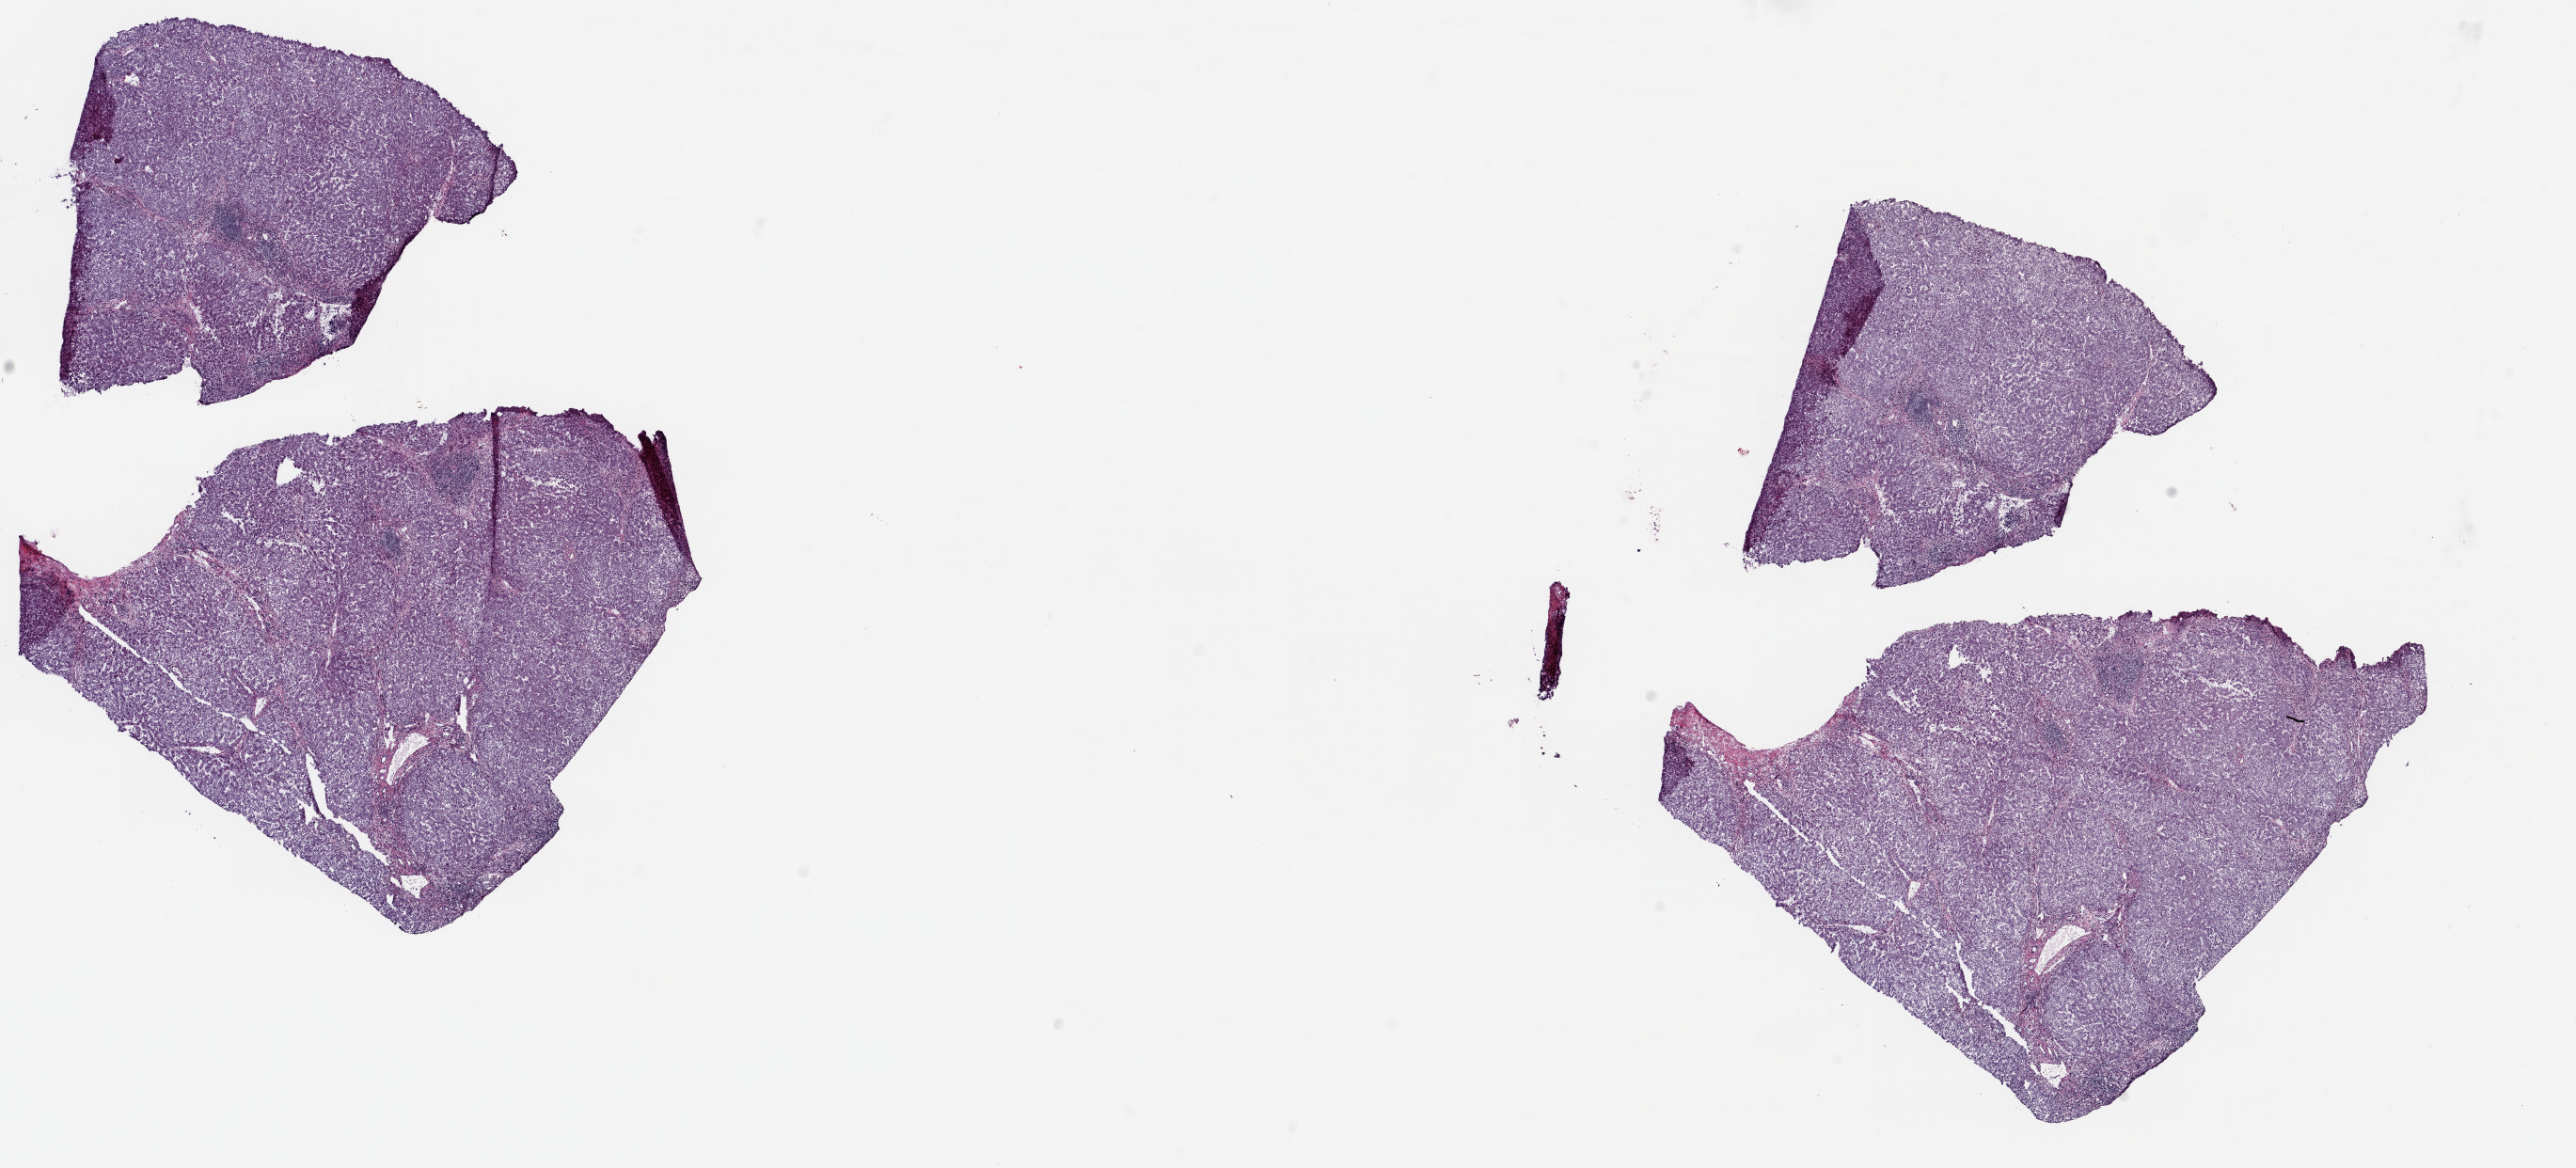
Digitized H&E tissue section (whole slide), whole scanned area (about 21.8 x 9.9 mm, slide scanned at 20x) shown as a low-resolution overview; frozen section from the top of the tissue portion; liver, solid tissue normal (non-tumour tissue) sample. Male, age 42 years at initial diagnosis. Composition of this section per pathologist review: tumour cells 0%, tumour nuclei 0%, normal cells 90%, stromal cells 10%, necrosis 0%. Infiltration values recorded for this section: lymphocyte infiltration 1%, monocyte infiltration 0%, neutrophil infiltration 0%.
* this section: solid tissue normal sample (biorepository sample class)
* patient diagnosis: Hepatocellular carcinoma, NOS